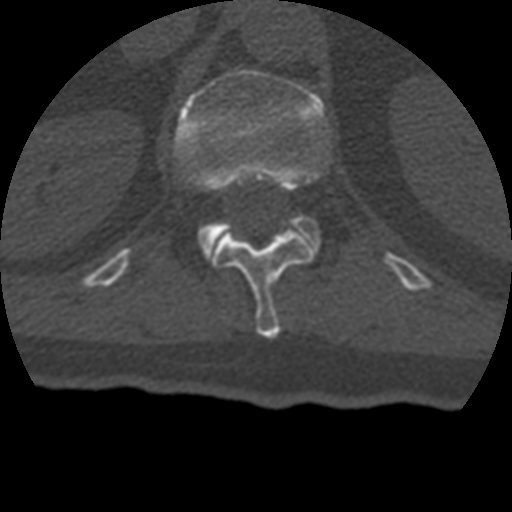
CT including the spine, one axial slice; slice 161 of 399 in the series (ordered by position); reconstruction kernel STANDARD; bone window (W 1800 / L 400 HU); 1.25 mm slice thickness; 512 × 512 image matrix, field of view 160 × 160 mm. Patient age 69 years. Case-level facts recorded for this patient, not image findings: primary cancer: prostate.
Outlined on this slice (semi-automatic segmentation, software-assisted and operator-edited):
- L1 vertebra: bounding box [x1, y1, x2, y2] px = [174, 69, 329, 260]
- T12 vertebra: [214, 182, 315, 338]